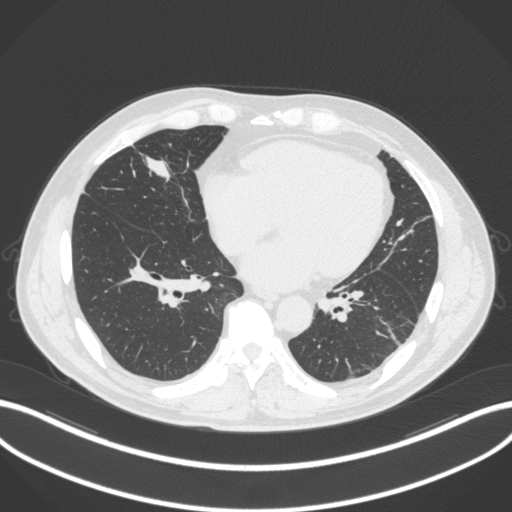
Chest CT, one axial slice; lung window (W 1500 / L -600 HU); 512 × 512 image matrix, field of view 400 × 400 mm. Patient: male, 59 years. From the clinical record (not read from this slice): clinical TNM (as recorded): T2a N1 M0.
Outlined on this slice (bounding box drawn by a radiologist):
- lung tumour (recorded histology: adenocarcinoma): bounding box [x1, y1, x2, y2] px = [139, 146, 176, 189]